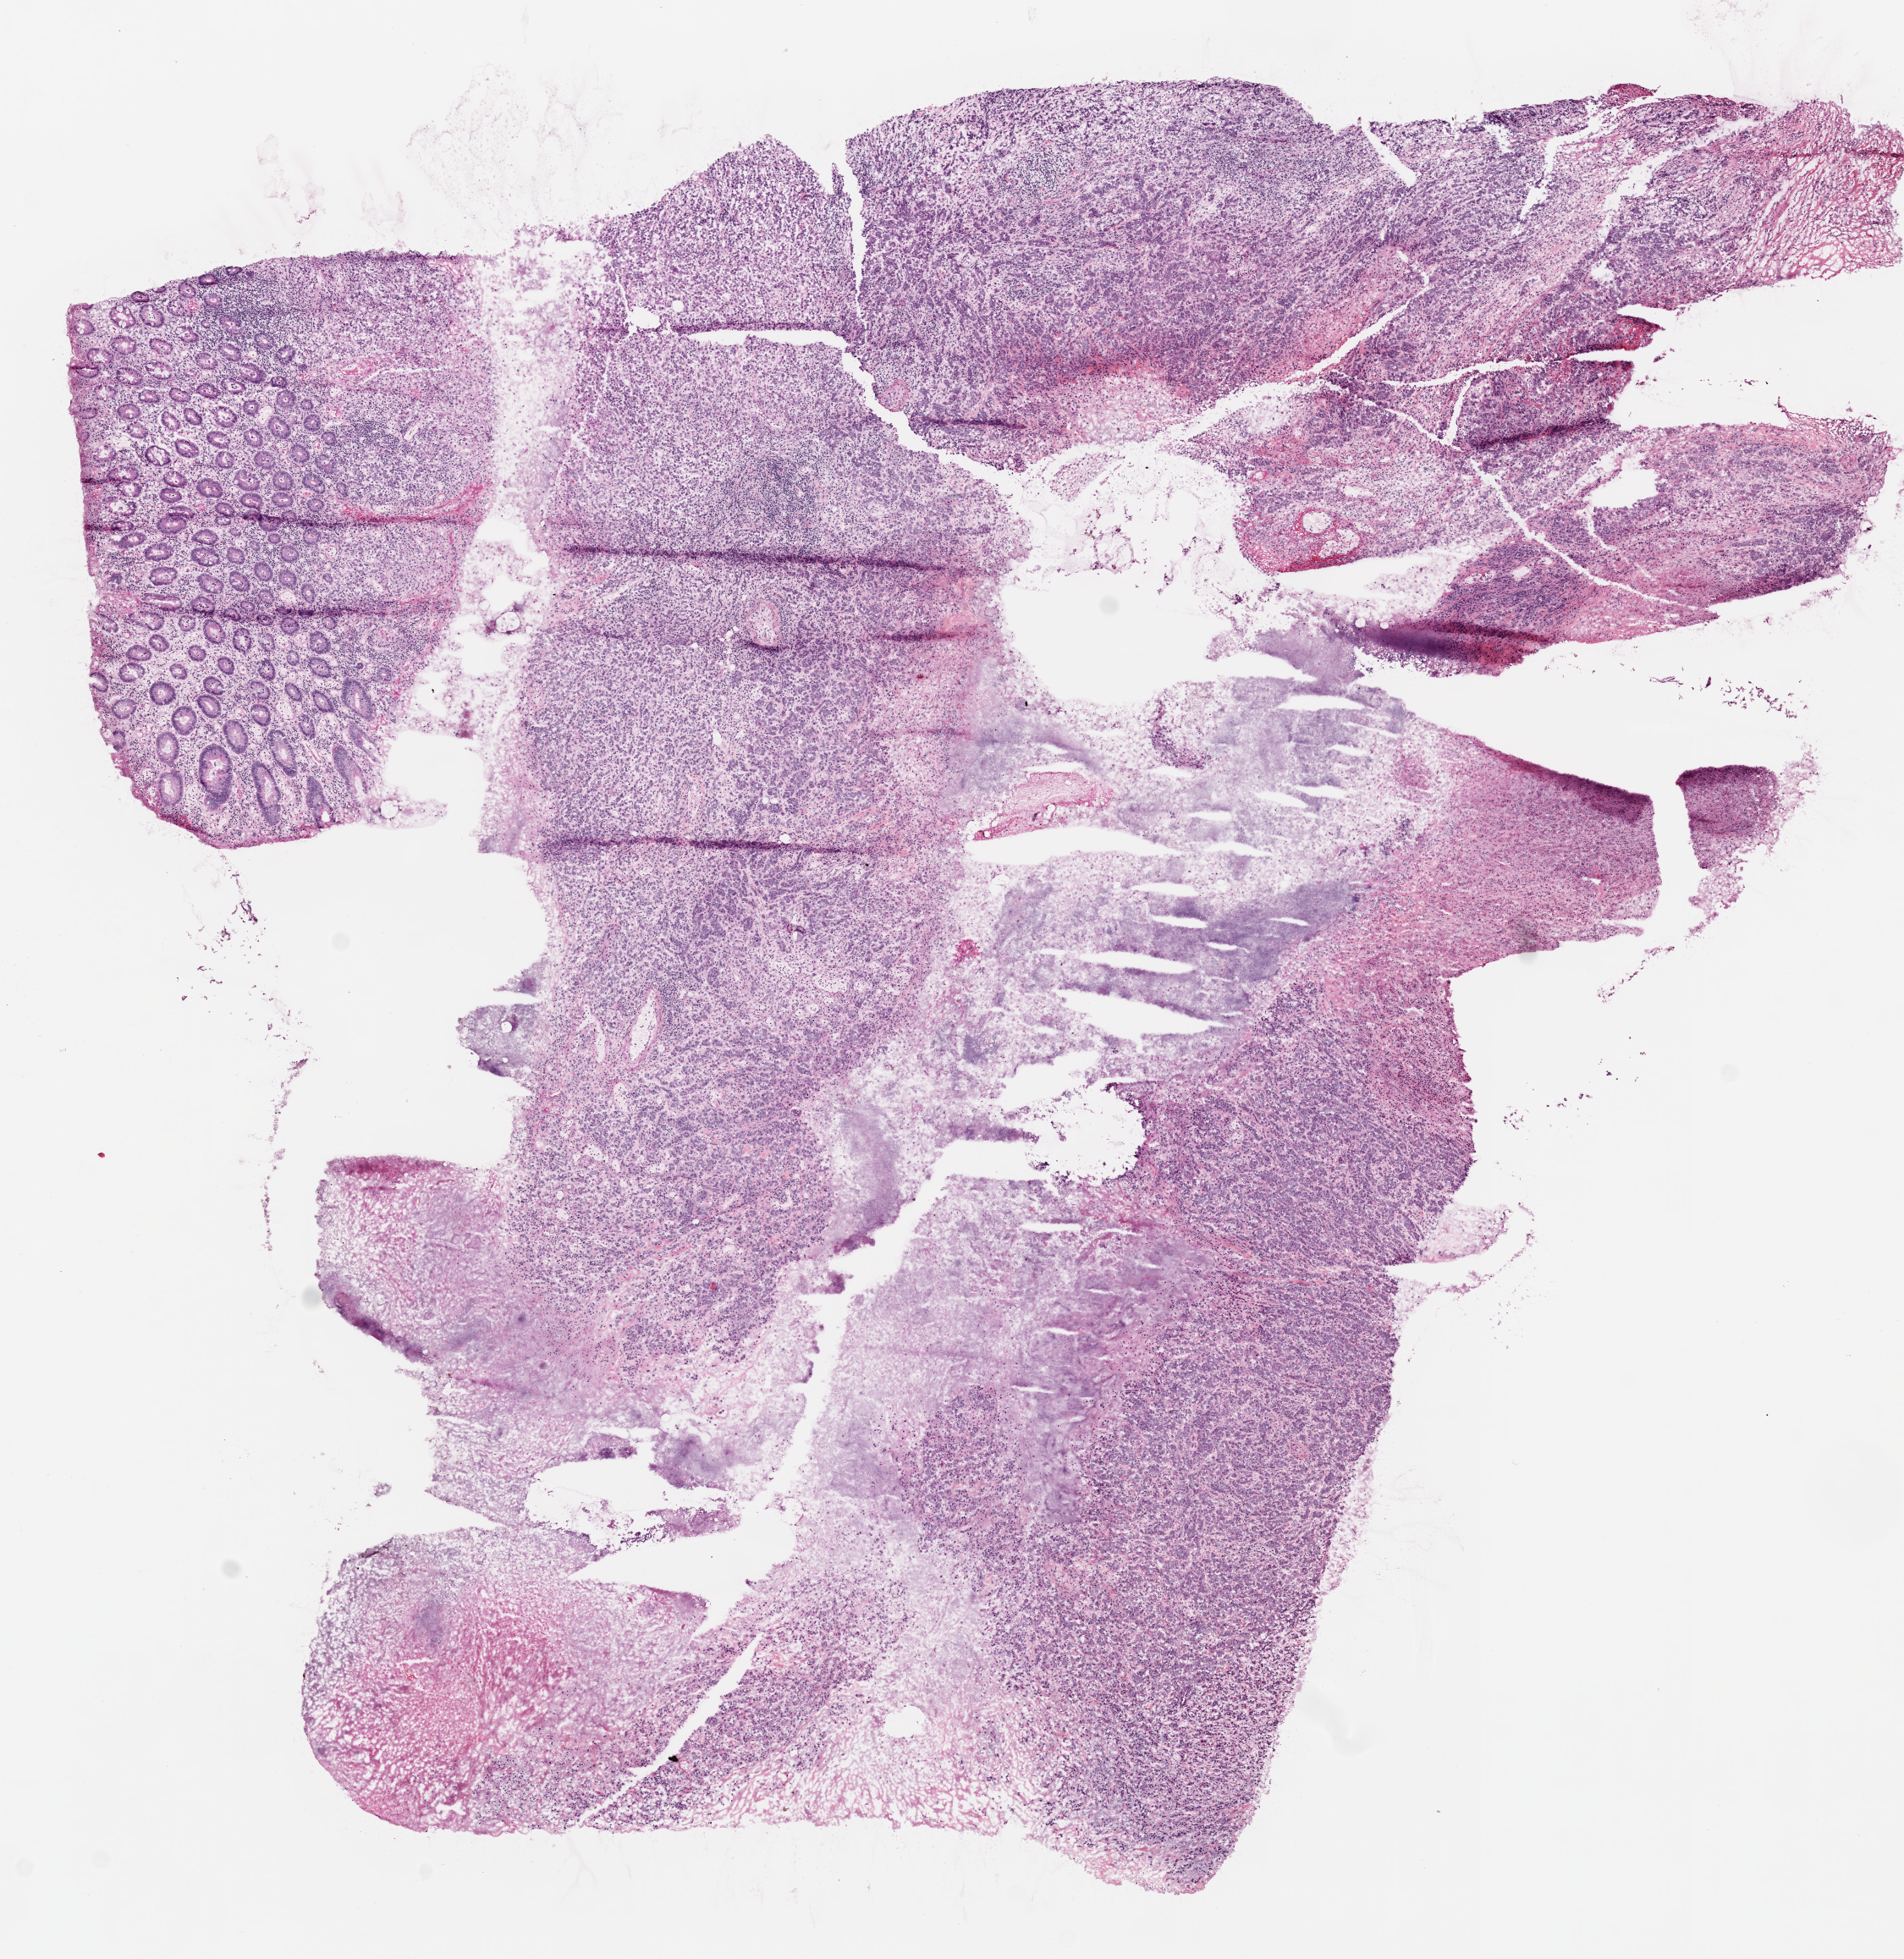
Hematoxylin and eosin (H&E) stained whole-slide image — a low-resolution overview of the entire scanned area, about 9.0 x 9.3 mm (slide scanned at 20x), frozen section from the top of the tissue portion, colon, primary tumour sample. Patient: female, age at initial diagnosis 68 years. Slide review estimates, as recorded: tumour cells 77%, tumour nuclei 75%, normal cells 8%, stromal cells 10%, necrosis 5%.
• pathologic diagnosis: Adenocarcinoma, NOS (sigmoid colon)
• TNM: T3 N0 M0
• AJCC pathologic stage: IIA (7th edition)